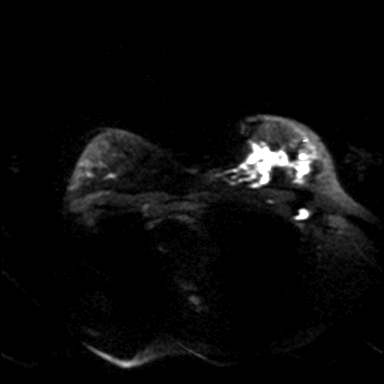
Breast MRI, one axial slice; slice 30 of 36 in the series (ordered by position); diffusion-weighted series; image 2 of 4 stored at this slice position (different b-values; order by instance number); 3 T; 384 × 384 image matrix. Female patient.
Structures marked on this image (outlined manually by an expert reader):
- tumour on diffusion-weighted imaging: bounding box [x1, y1, x2, y2] px = [297, 159, 311, 172]